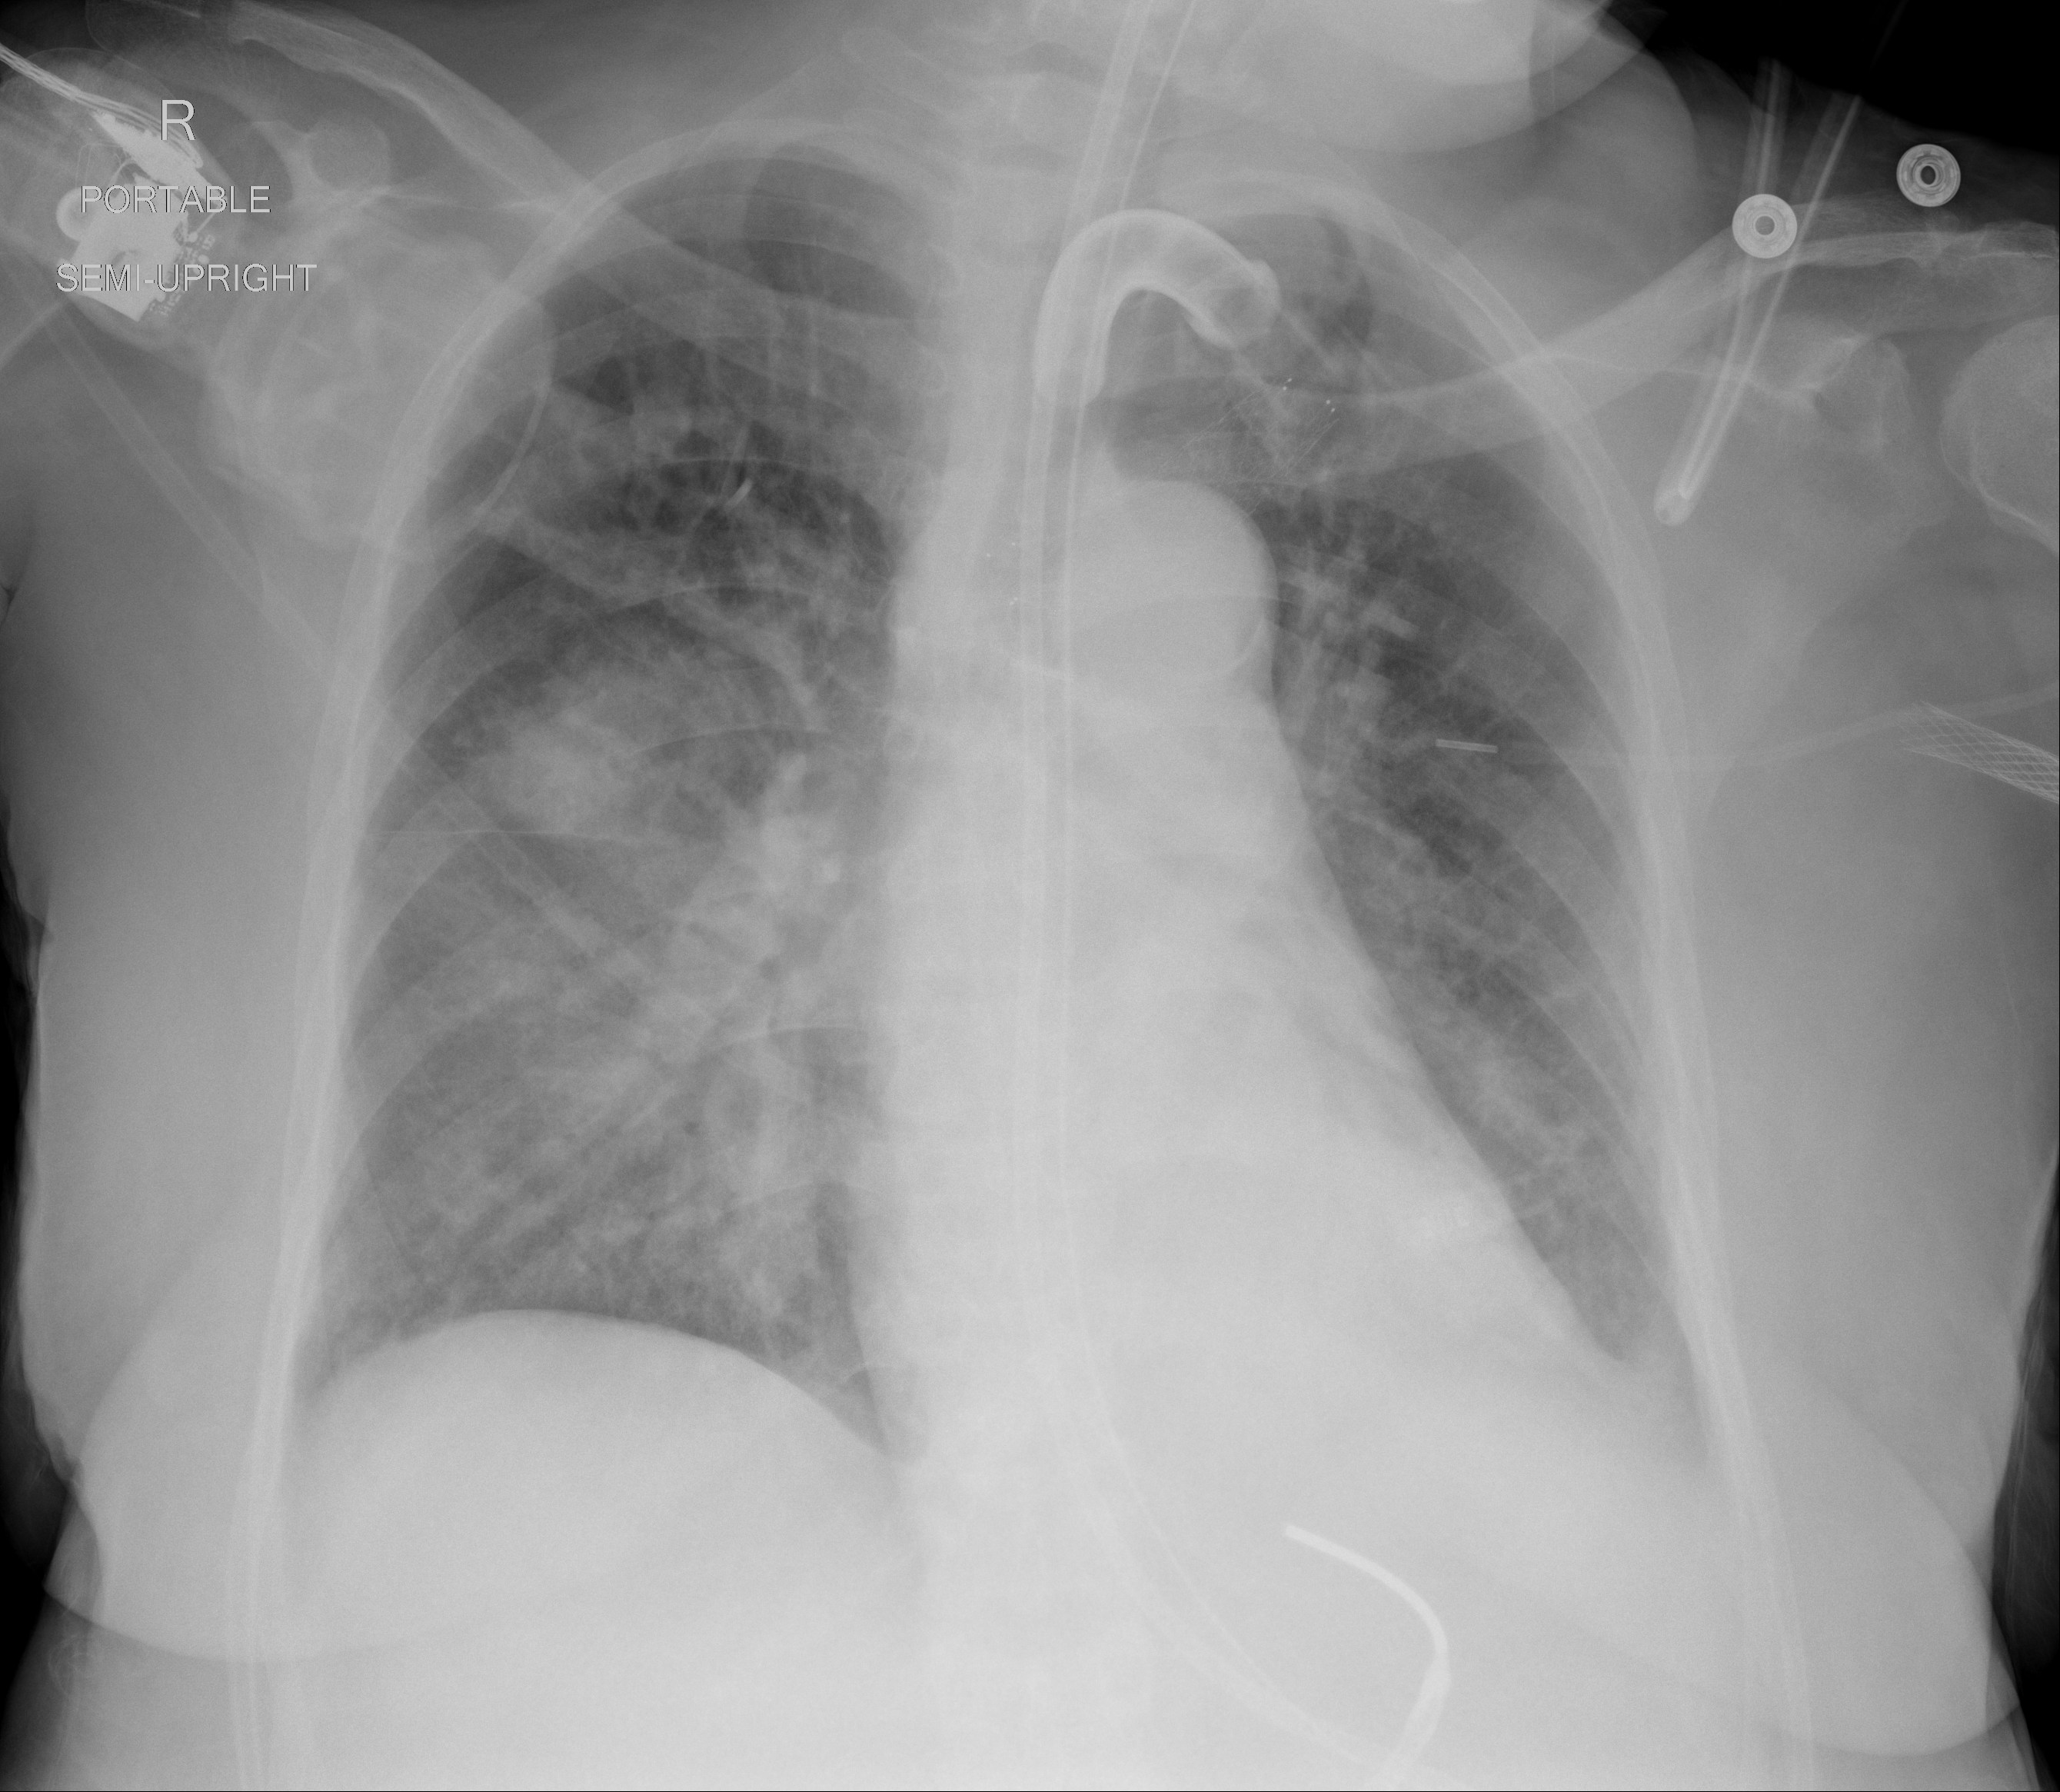
Portable chest radiograph, AP projection. Female patient, age 64 years; imaged 22 days after the COVID-19 diagnosis.
Radiologist key findings (as recorded): ill-defined bilateral airspace opacities within the central mid to lower lungs.